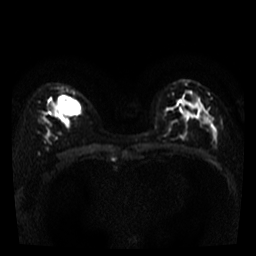
Breast MRI, one axial slice. Position 24 of 40 along the scan axis. Diffusion-weighted series; image 2 of 4 stored at this slice position (different b-values; order by instance number). 3 T. 5 mm slice thickness. 256 × 256 image matrix. Female patient.
Structures marked on this image (outlined manually by an expert reader):
- tumour on diffusion-weighted imaging: box from (x=58, y=97) to (x=79, y=114) px